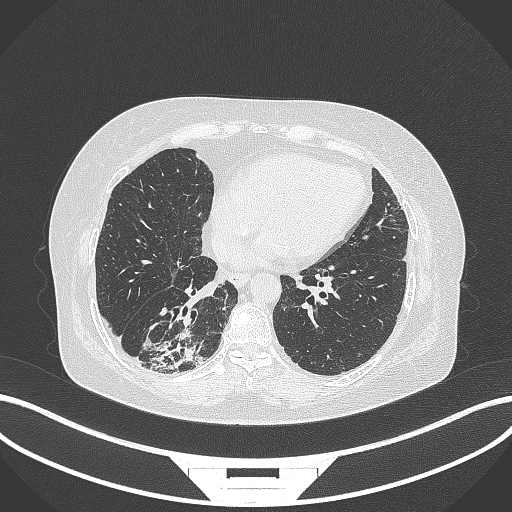
Chest CT, one axial slice. Position 79 of 296 along the scan axis. Reconstruction kernel B70f. Lung window (W 1500 / L -600 HU). 512 × 512 image matrix, field of view 400 × 400 mm. Female patient, age 65 years. Case-level facts recorded for this patient, not image findings: clinical TNM (as recorded): T2b N1 M0.
Outlined on this slice (rectangle marked by the reading radiologist):
- lung tumour (recorded histology: adenocarcinoma): bounding box <140,316,211,375> (left, top, right, bottom; pixels)